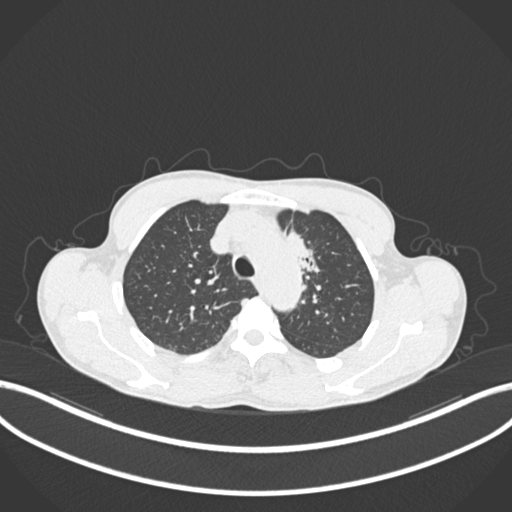
Chest CT, one axial slice; reconstruction kernel B30f; 120 kVp; lung window (W 1500 / L -600 HU); 1 mm slice thickness; 512 × 512 image matrix, field of view 400 × 400 mm. Patient: male, 58 years. From the clinical record (not read from this slice): clinical TNM (as recorded): T1c N1 M0.
Annotated regions visible in this slice (bounding box drawn by a radiologist):
- lung tumour (recorded histology: adenocarcinoma): bounding box [x1, y1, x2, y2] px = [284, 230, 326, 279]